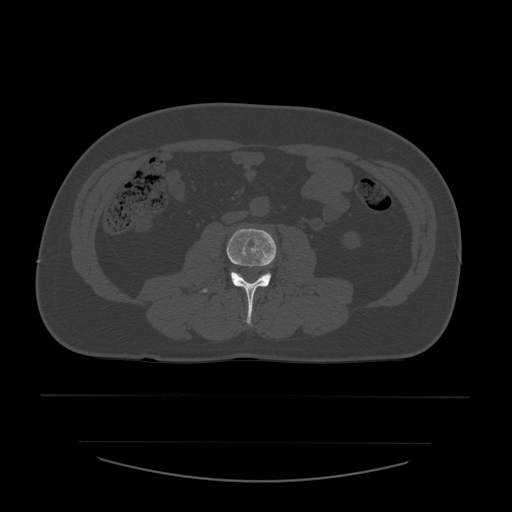
CT including the spine, one axial slice. Reconstruction kernel STANDARD. 120 kVp. Bone window (W 1800 / L 400 HU). 512 × 512 image matrix. Patient age 44 years. Case-level facts recorded for this patient, not image findings: primary cancer: soft tissue sarcoma.
Structures marked on this image (semi-automatic segmentation, software-assisted and operator-edited):
- L3 vertebra: bounding box (x1, y1, x2, y2) in pixels: (200, 229, 277, 324)